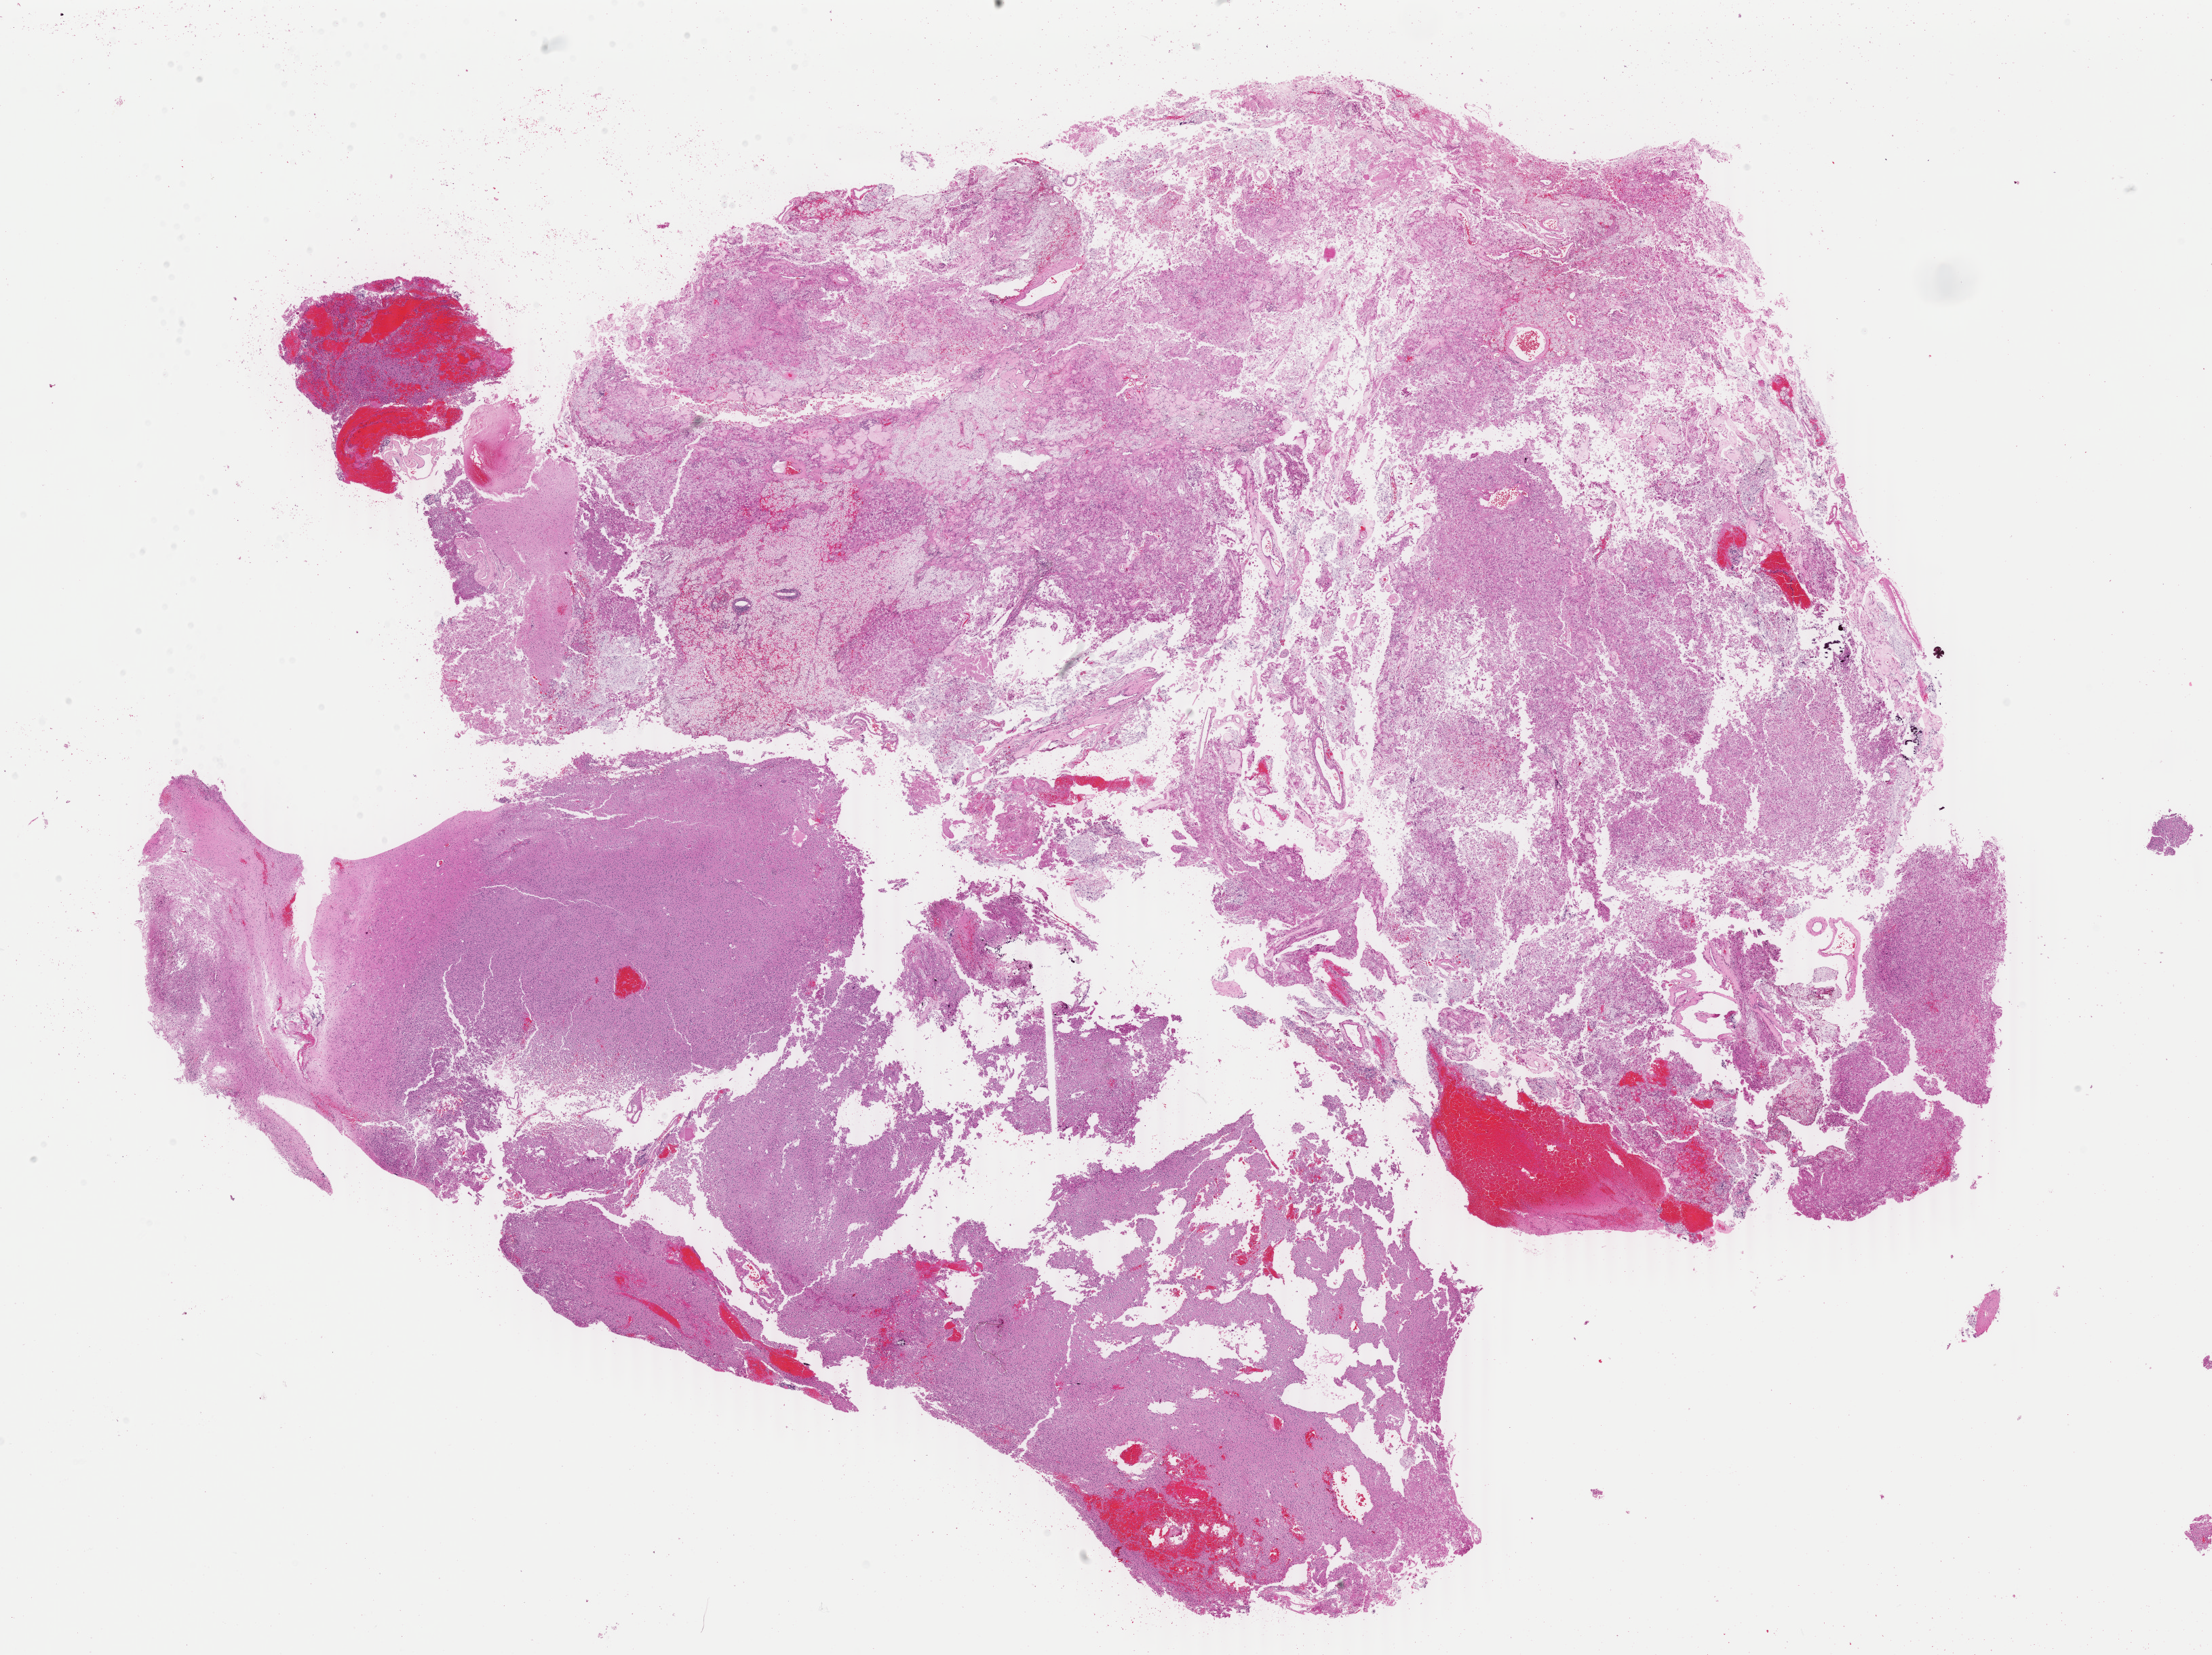
Digitized Hematoxylin and eosin (H&E) stained tissue section (whole slide), whole scanned area (about 25.9 x 19.4 mm, acquisition: 40x scan) shown as a low-resolution overview. Formalin-fixed paraffin-embedded (FFPE) diagnostic section. Brain, primary tumour sample. Patient: male, age at initial diagnosis 68 years.
* histologic diagnosis: Glioblastoma